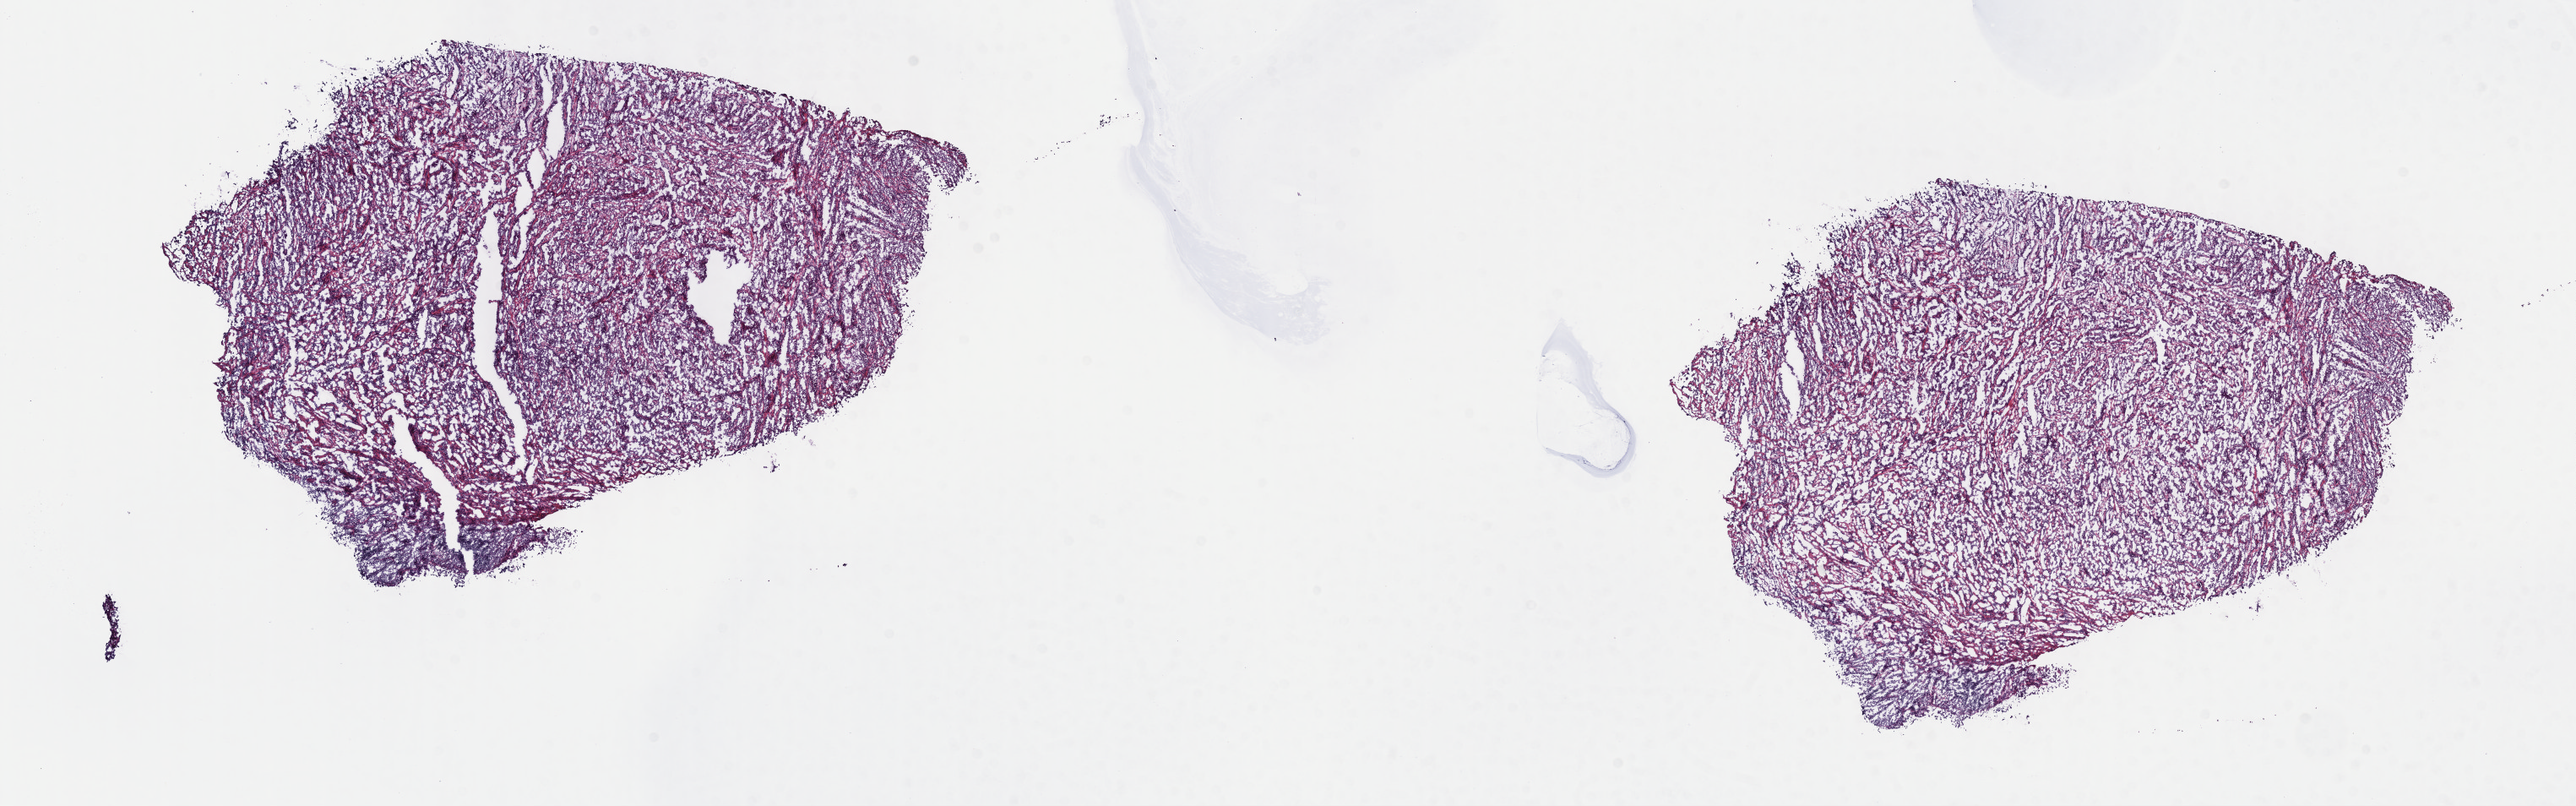
Whole-slide histology image, H&E-stained — a low-resolution overview of the entire scanned area, about 24.7 x 7.7 mm (slide scanned at 40x); frozen section from the top of the tissue portion; primary tumour sample from the mesothelium. Female, age 71 years at initial diagnosis. Composition of this section per pathologist review: tumour cells 100%, tumour nuclei 70%, normal cells 0%, stromal cells 0%, necrosis 0%. Infiltration values recorded for this section: lymphocyte infiltration 2%, monocyte infiltration 0%, neutrophil infiltration 0%.
• diagnosis: Epithelioid mesothelioma, malignant
• AJCC pathologic stage: IV (7th edition)